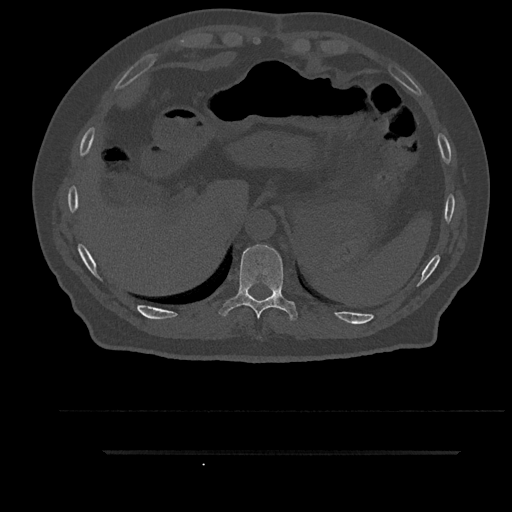
CT including the spine, one axial slice; position 366 of 797 along the scan axis; bone window (W 1800 / L 400 HU); 0.5 mm slice thickness; 512 × 512 image matrix, field of view 432 × 432 mm. Male patient, age 63 years. From the clinical record (not read from this slice): primary cancer: renal.
Structures marked on this image (semi-automatically segmented with operator editing):
- T10 vertebra: bounding box <219,244,298,321> (left, top, right, bottom; pixels)